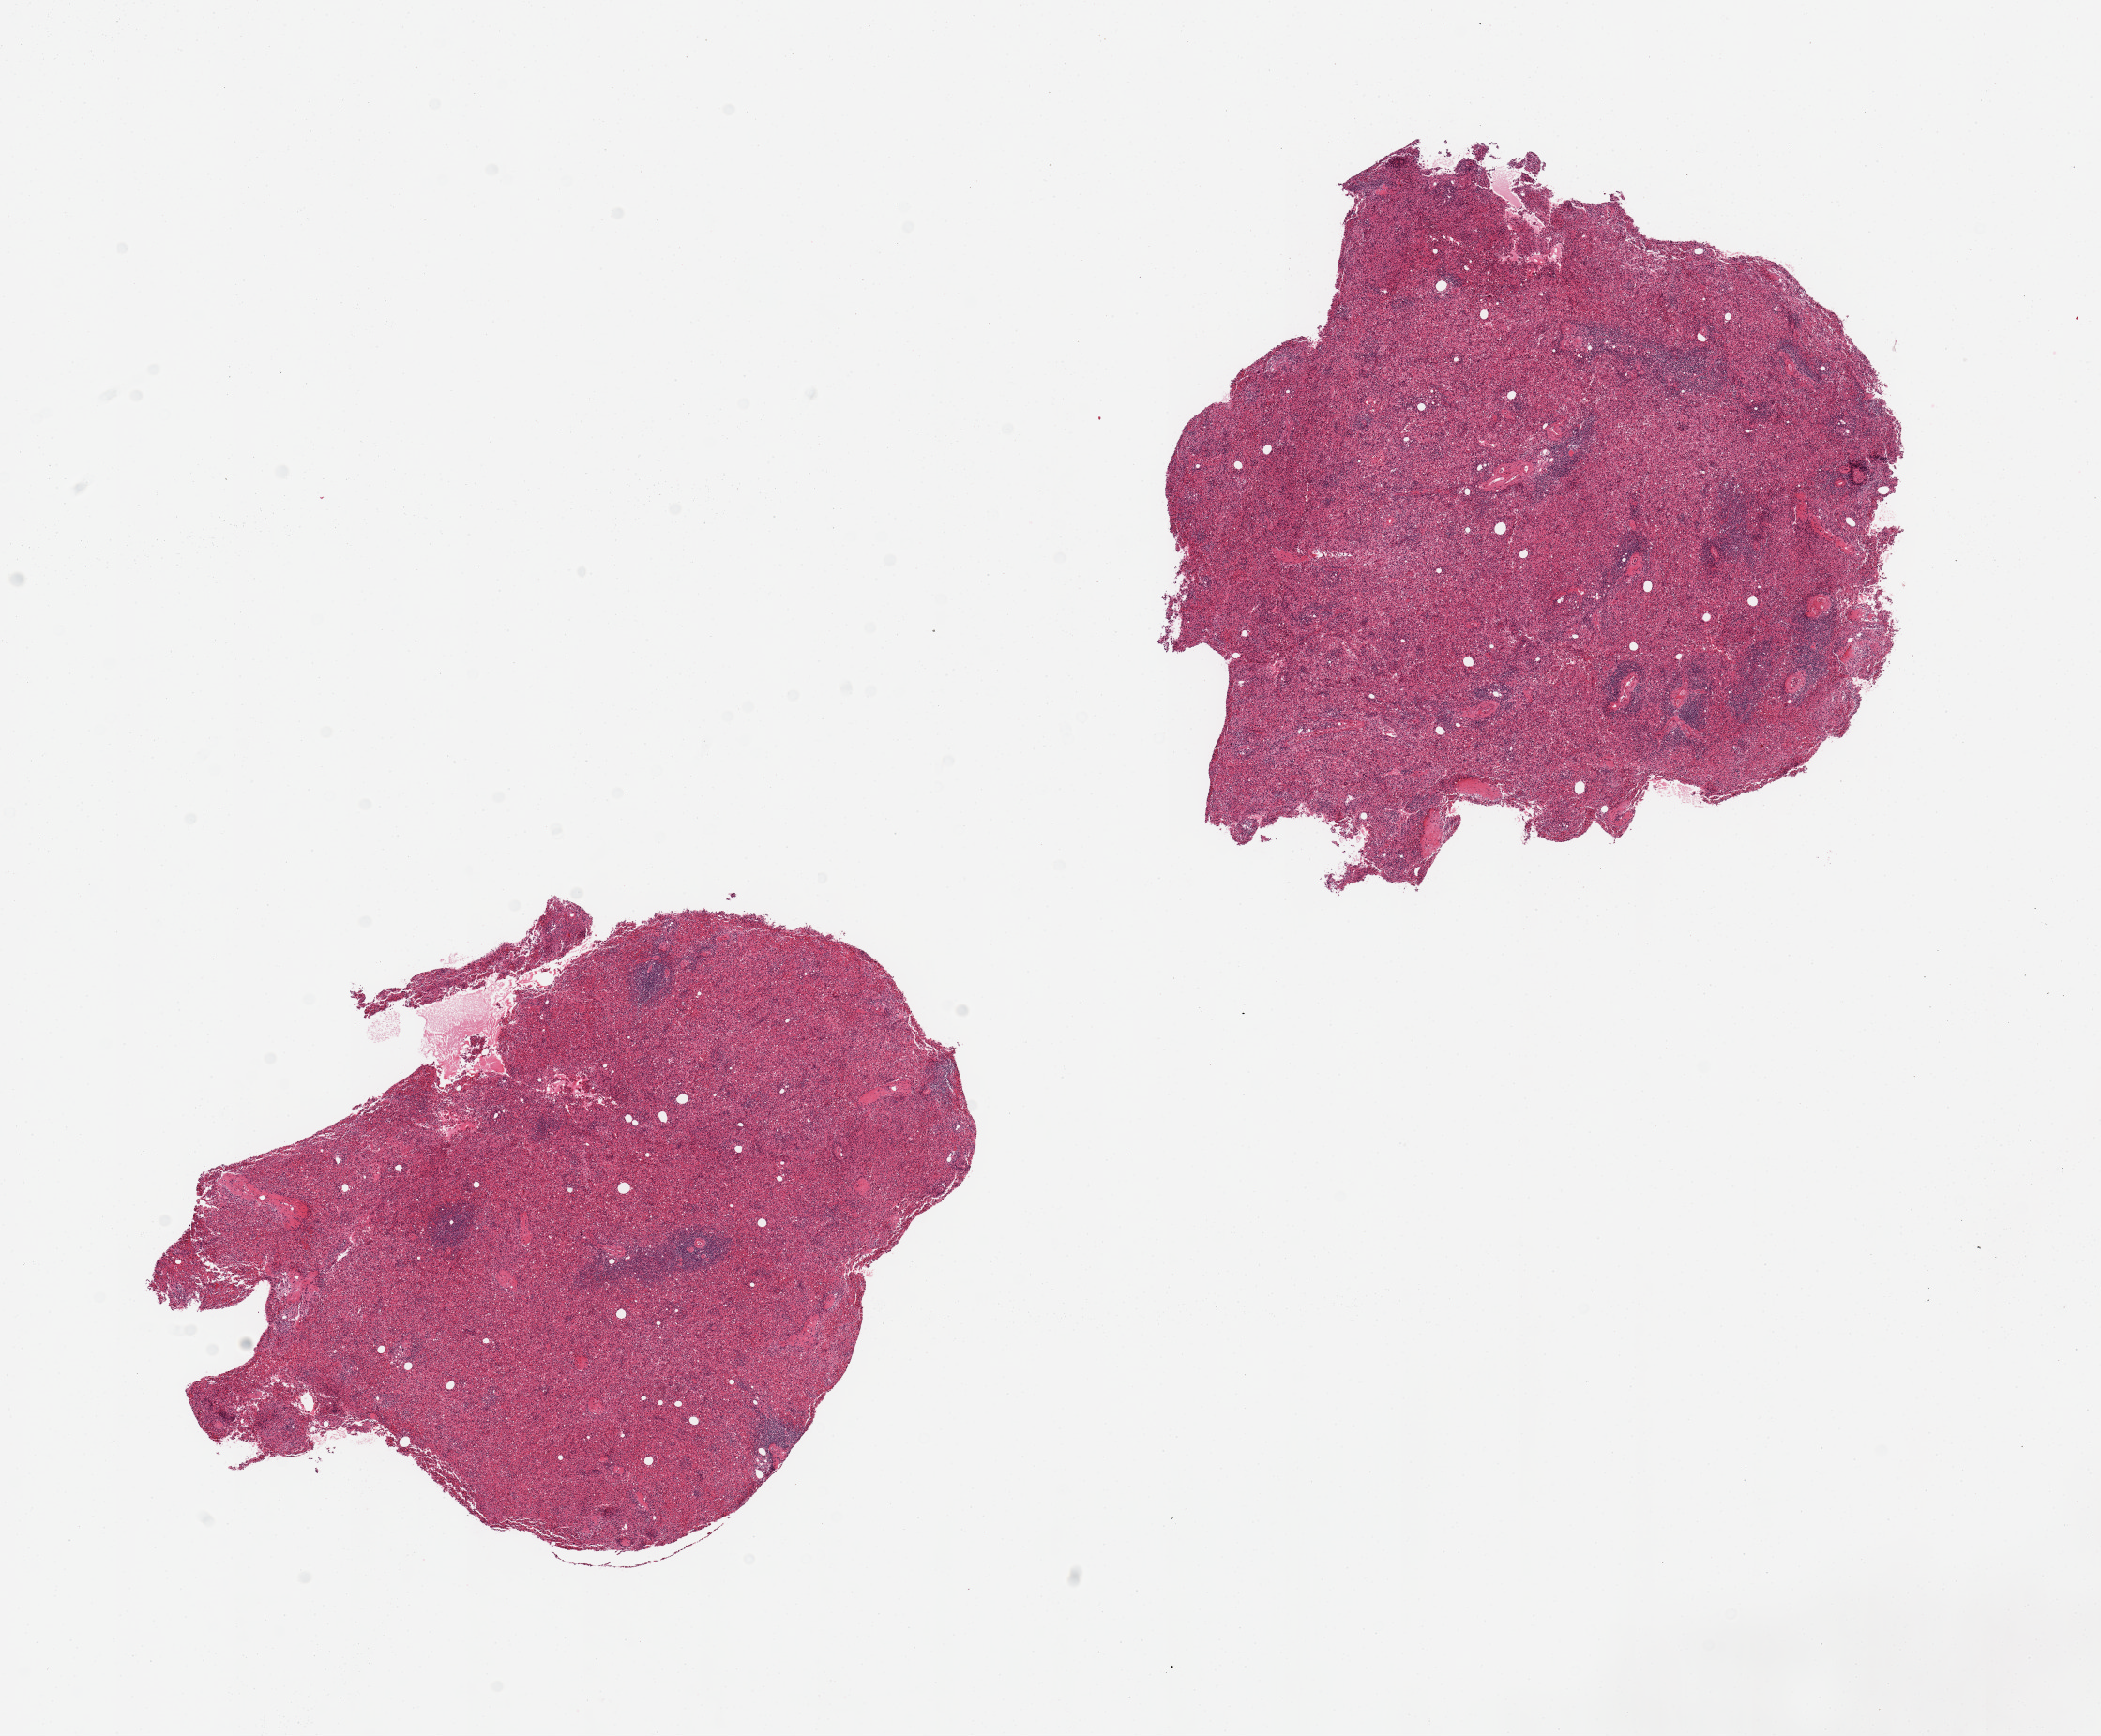
Hematoxylin and eosin (H&E) whole-slide image, brightfield, whole scanned area (about 17.7 x 14.6 mm, acquisition: 20x scan) shown as a low-resolution overview, PAXgene-fixed, paraffin-embedded tissue, target tissue: spleen, tissue donor sample. Donor: male.
Reviewer comment on this tissue sample: 2 pieces, no significant abnormalities.